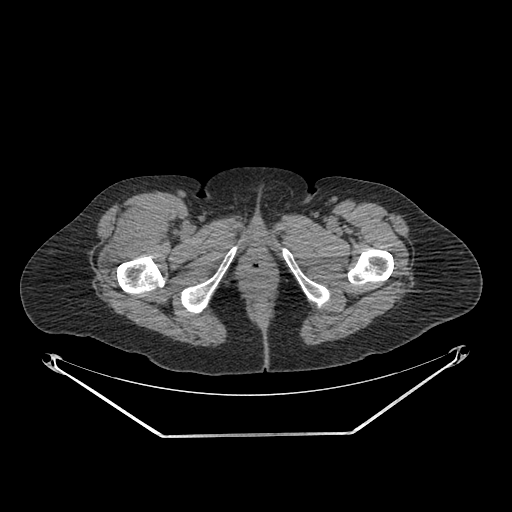
CT of an extremity soft-tissue mass (from a PET/CT study), one axial slice; position 280 of 311 along the scan axis; 140 kVp; soft-tissue window (W 400 / L 40 HU); 3.75 mm slice thickness; 512 × 512 image matrix, field of view 500 × 500 mm. Female patient. From the clinical record (not read from this slice): histological type: pleiomorphic undifferentiated sarcoma; grade: high; site of the primary tumour: right quadricep.
Structures marked on this image (expert contour drawn on MRI and transferred to this co-registered scan by the dataset authors):
- tumour plus oedema (research contour): bounding box [x1, y1, x2, y2] px = [101, 203, 168, 270]
- tumour (research contour): [103, 203, 168, 268]